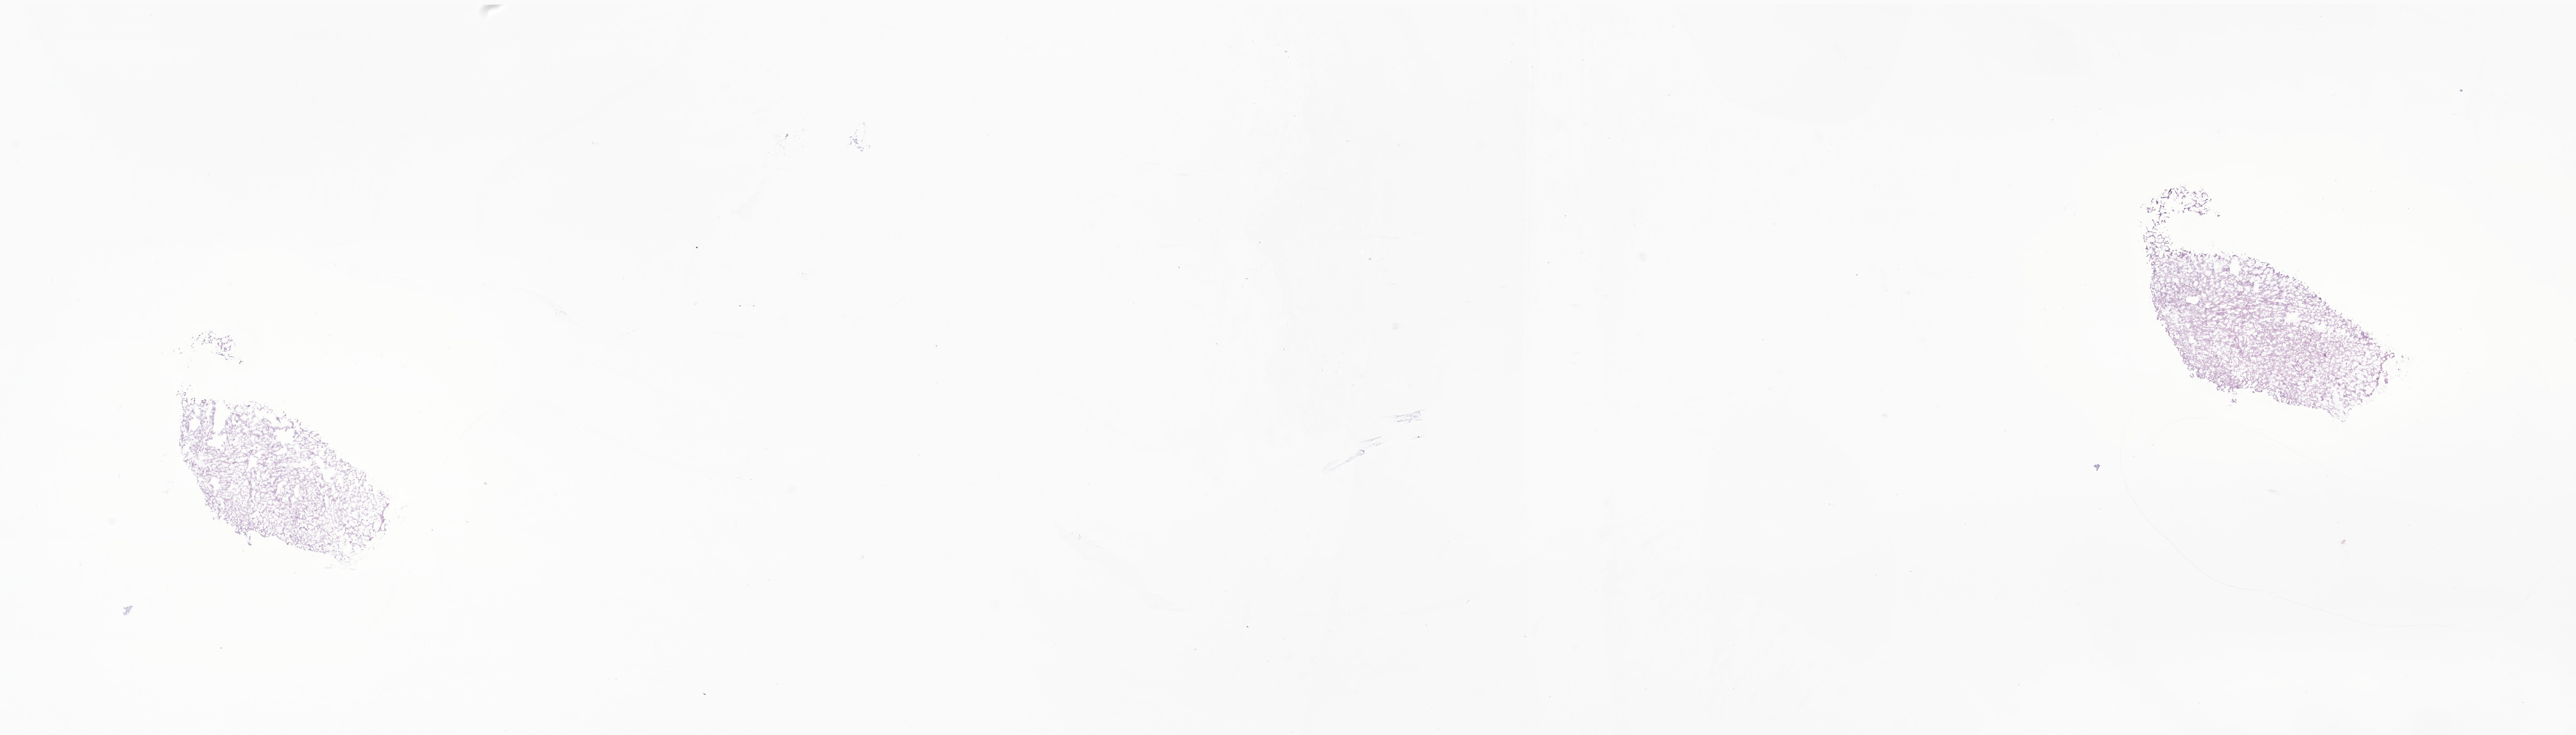
Digitized hematoxylin and eosin (H&E)-stained section of tumor tissue from the brain stem, whole scanned area (about 27.5 x 7.8 mm) shown as a low-resolution overview. Cryosection (OCT / tissue freezing medium). Male patient, age 81 months (6 years 9 months).
Diagnosis (ICD-O-3 morphology term): Glioma, malignant.